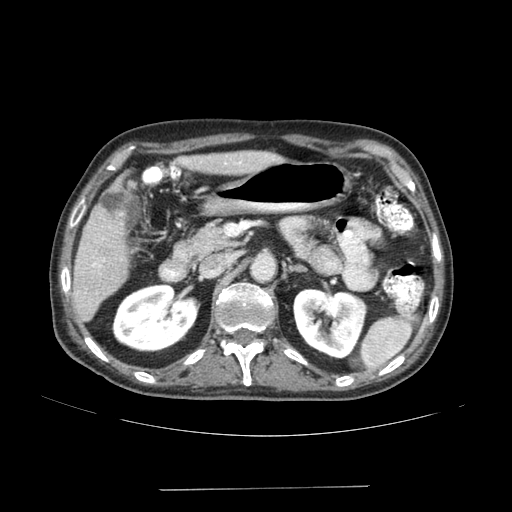
Contrast-enhanced abdominal CT (liver protocol), one axial slice. Slice 74 of 192 in the series (ordered by position). 120 kVp. Soft-tissue window (W 400 / L 40 HU). 2.5 mm slice thickness. 512 × 512 image matrix, field of view 400 × 400 mm. From the clinical record (not read from this slice): diagnosis: hepatocellular carcinoma (patient treated with transarterial chemoembolisation; whether this scan precedes or follows treatment is not stated here); TNM stage (as recorded): Stage-IVA; Child-Pugh class: A; tumour differentiation: poorly differentiated; tumour nodularity: uninodular.
Annotated regions visible in this slice (semi-automatic segmentation, software-assisted and operator-edited):
- liver parenchyma outside the tumour (the mass and vessels are separate outlines, so this box may not span the whole liver): bounding box <72,150,281,322> (left, top, right, bottom; pixels)
- liver vessels: <93,162,241,266>